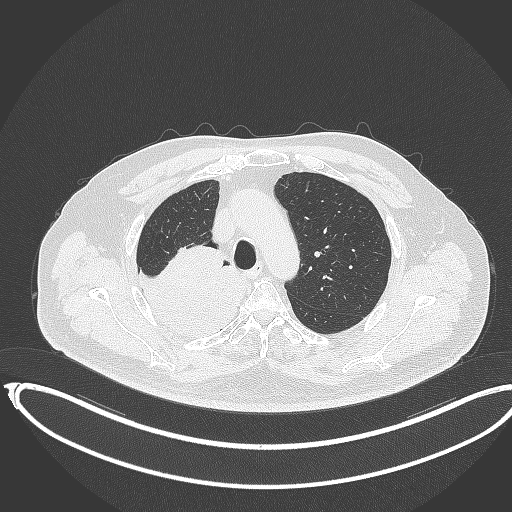
Chest CT, one axial slice. Reconstruction kernel B70f. Lung window (W 1500 / L -600 HU). 1 mm slice thickness. 512 × 512 image matrix. Patient: male, 68 years. From the clinical record (not read from this slice): clinical TNM (as recorded): T2a N0 M0.
Outlined on this slice (bounding box drawn by a radiologist):
- lung tumour (recorded histology: adenocarcinoma): box from (x=128, y=243) to (x=248, y=345) px